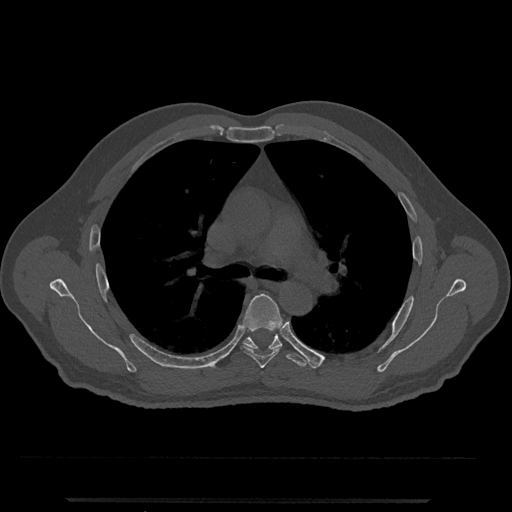
CT including the spine, one axial slice. Slice 771 of 797 in the series (ordered by position). Reconstruction kernel Br40s/3. Bone window (W 1800 / L 400 HU). 0.5 mm slice thickness. 512 × 512 image matrix. Patient: male, 63 years. Case-level facts recorded for this patient, not image findings: primary cancer: prostate.
Outlined on this slice (semi-automatically segmented with operator editing):
- T5 vertebra: bounding box [x1, y1, x2, y2] px = [241, 293, 282, 369]
- T6 vertebra: [243, 333, 307, 367]